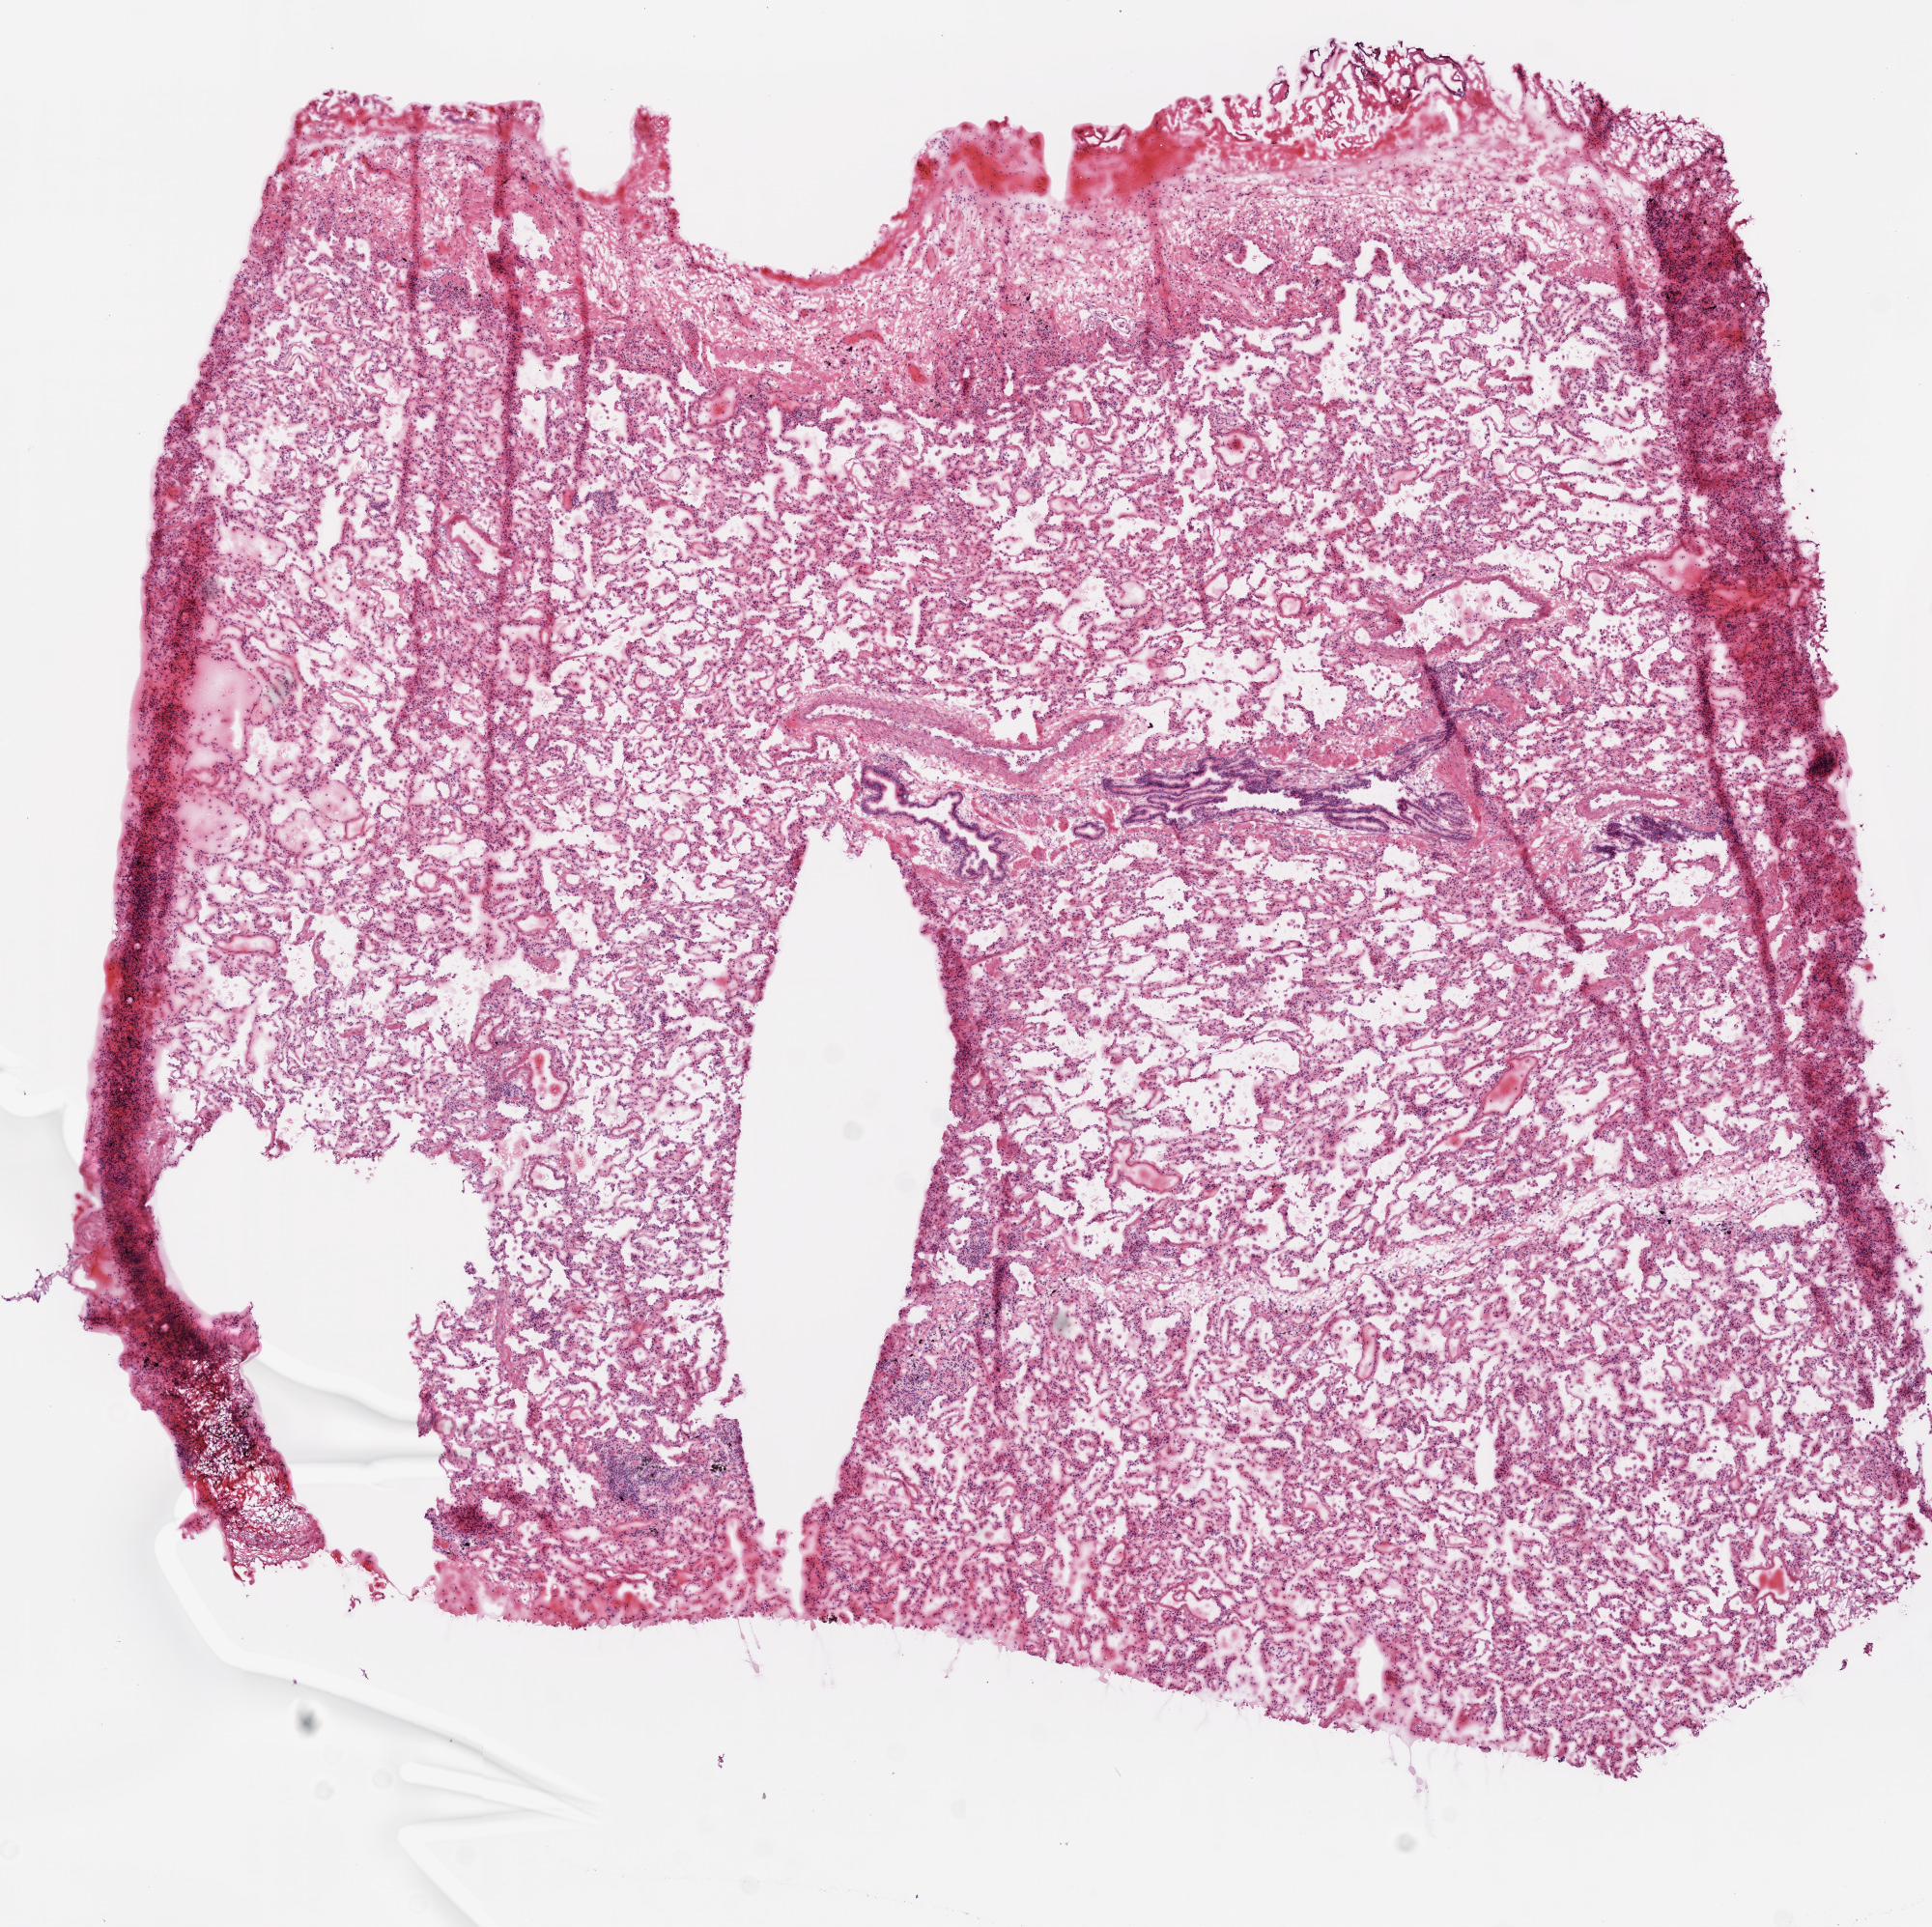
Whole-slide histology image, Hematoxylin and eosin (H&E) stained — whole scanned area (about 8.0 x 8.0 mm) shown as a low-resolution overview; frozen section; solid tissue normal (non-tumour tissue) sample from the lung. Patient: female, age at initial diagnosis 80 years.
- this section: solid tissue normal sample (biorepository sample class)
- patient diagnosis: Adenocarcinoma, NOS